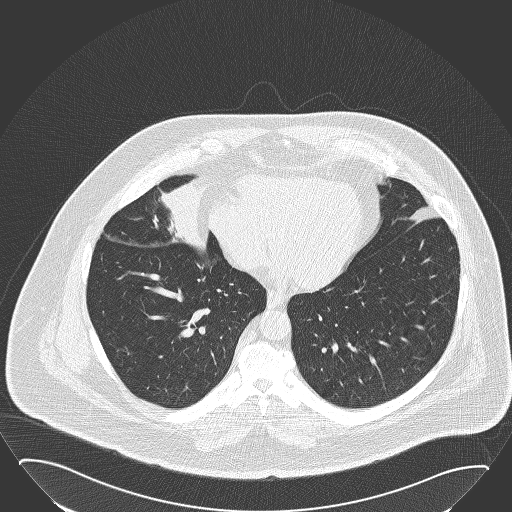
Low-dose screening chest CT, axial slice, baseline annual screen, lung window (W 1500 / L -600 HU), slice 107 of 168 in the series, 512 × 512 image matrix, field of view 432 × 432 mm. Male, age 61 years at enrolment.
Expert reader's lesion annotation, box from (x=130, y=165) to (x=226, y=255) px. The screening reader recorded 2 non-calcified nodules or masses ≥4 mm on this exam (right middle lobe, left lower lobe); which of them this box marks is not recorded. Official screen result: positive, change unspecified: nodule(s) >= 4 mm or enlarging nodule(s), mass(es), or other non-specific abnormalities suspicious for lung cancer. Later outcome: lung cancer diagnosed 47 days after this screen — basaloid squamous cell carcinoma, right middle lobe, right hilum, poorly differentiated (G3), stage IIB (AJCC 6th edition), 95 mm at pathology.